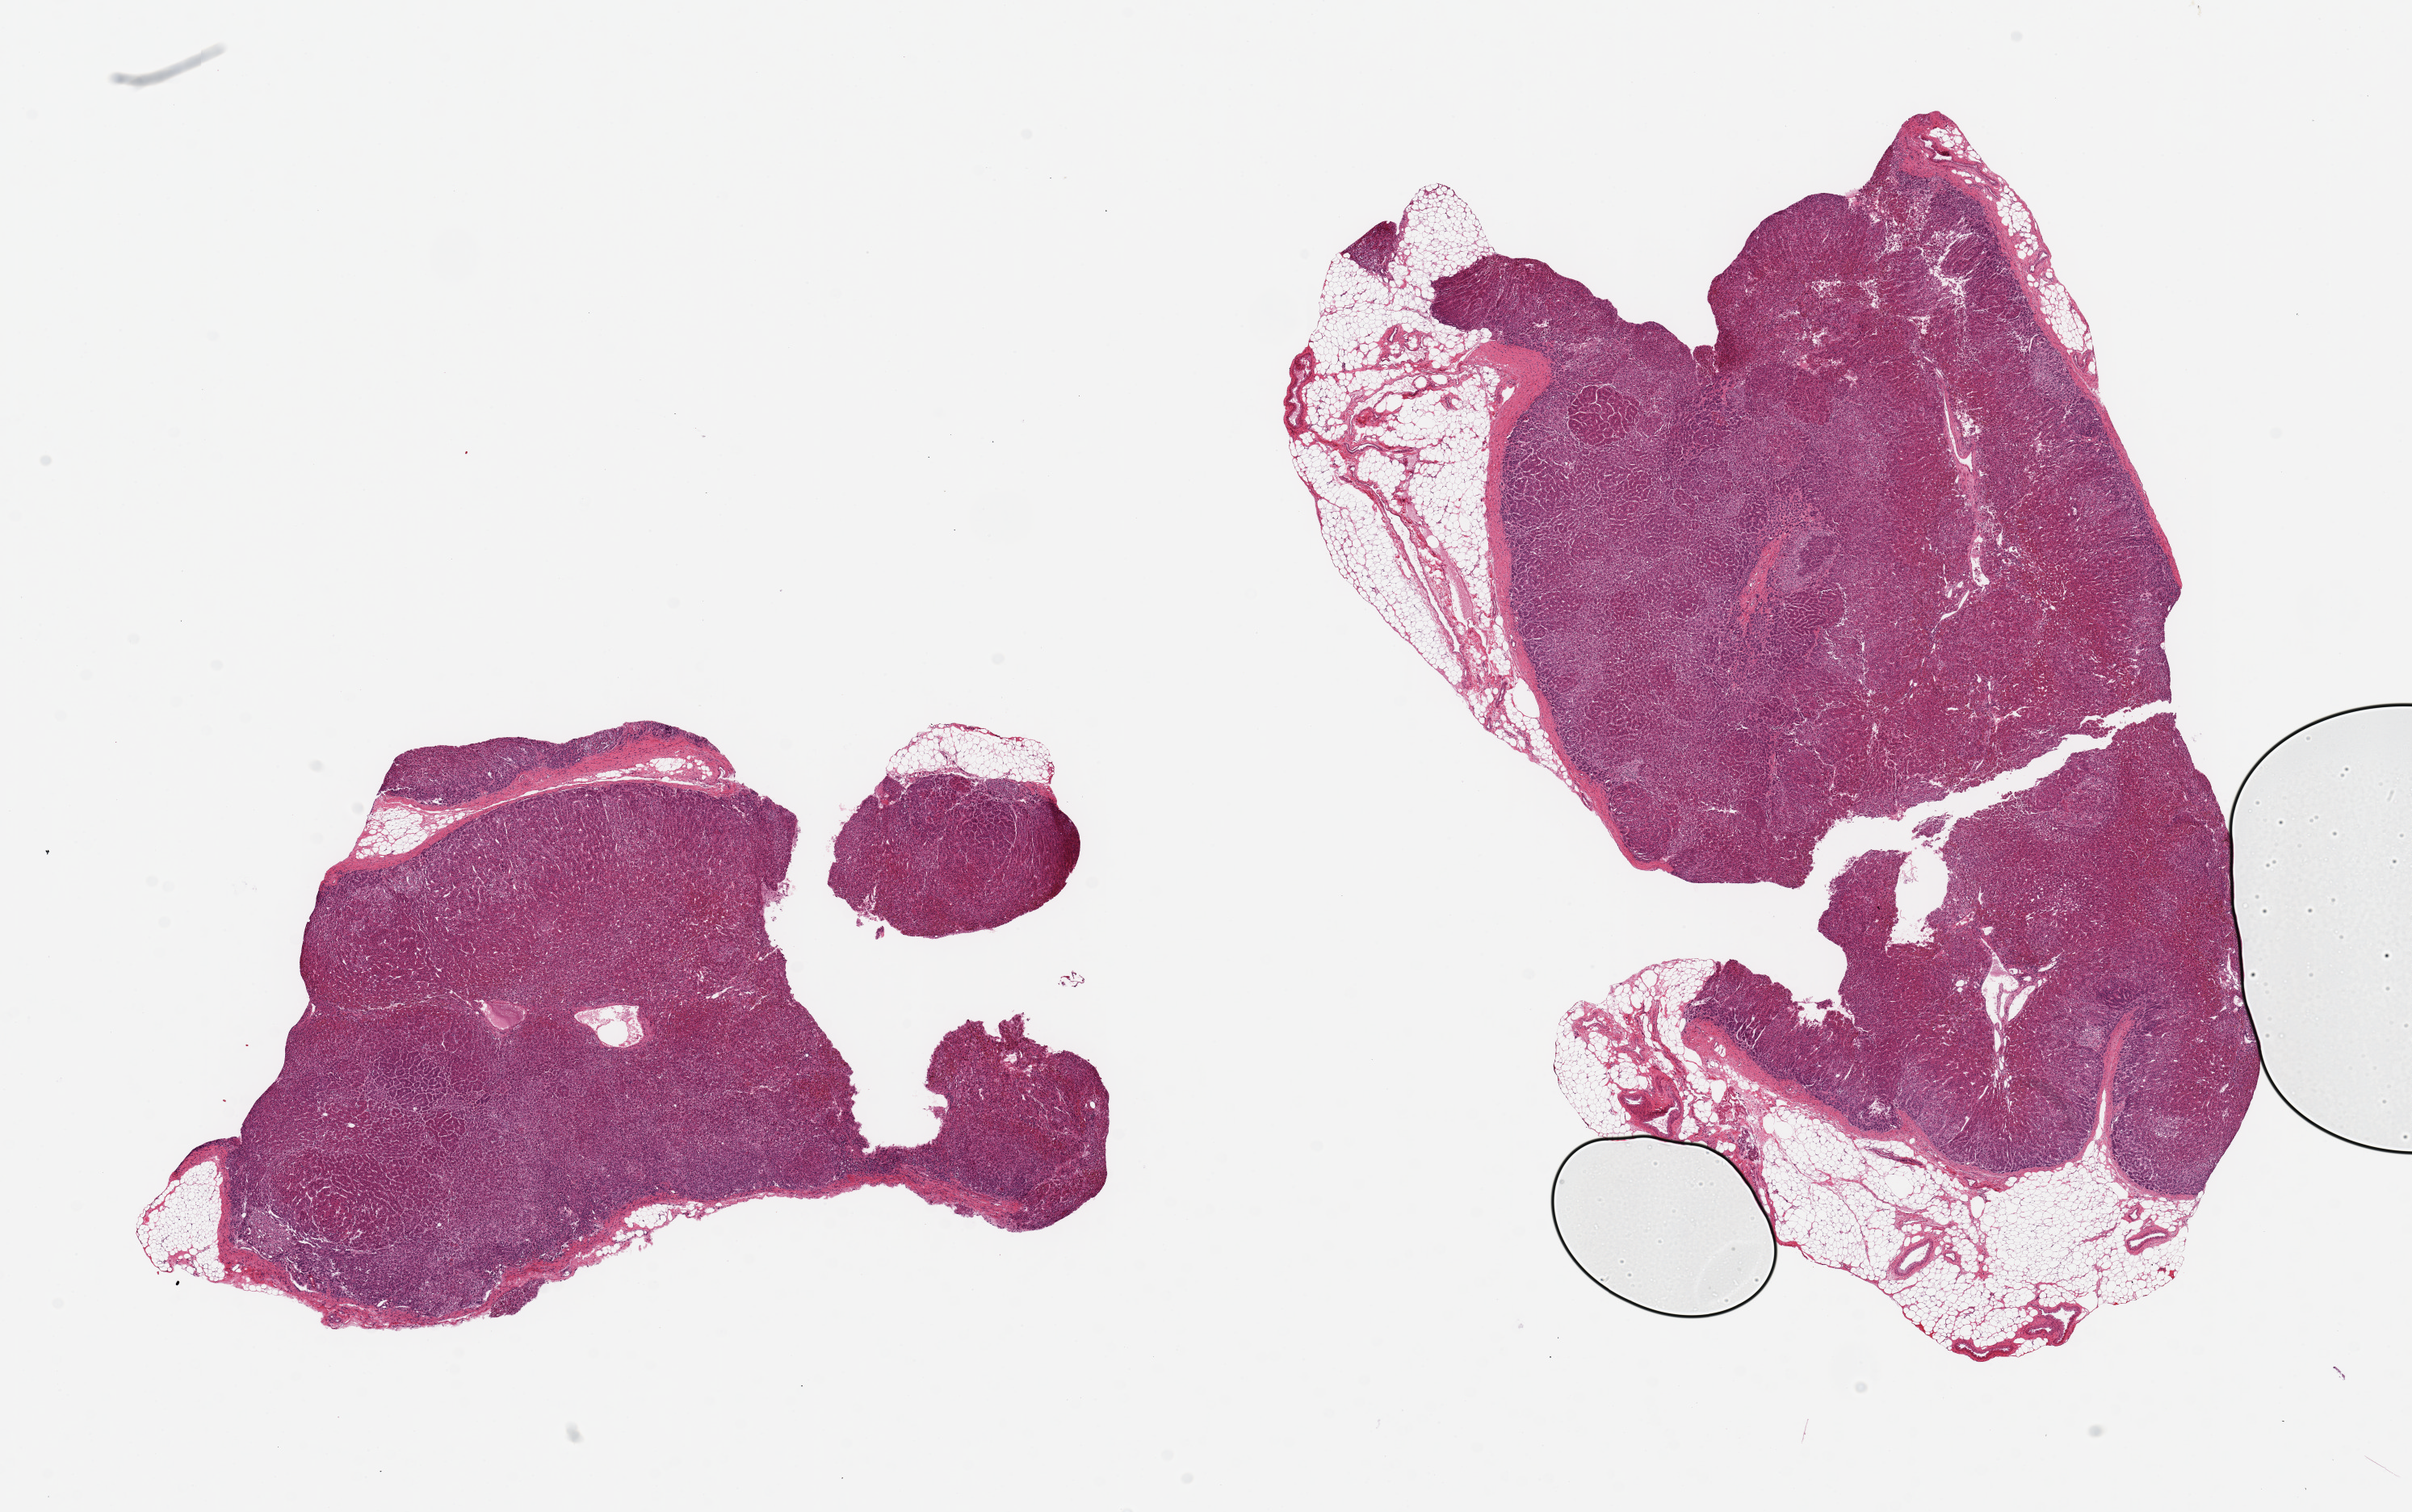
Digitized H&E-stained section, brightfield — a low-resolution overview of the entire scanned area, about 23.6 x 14.8 mm. PAXgene-fixed, paraffin-embedded tissue. Section of adrenal gland (target tissue). Tissue donor sample. Donor sex: female.
Reviewer comment on this tissue sample: 2 pieces ~9x6mm; Well-preserved, ~15% of larger aliquot is nubbins of adherent fat.